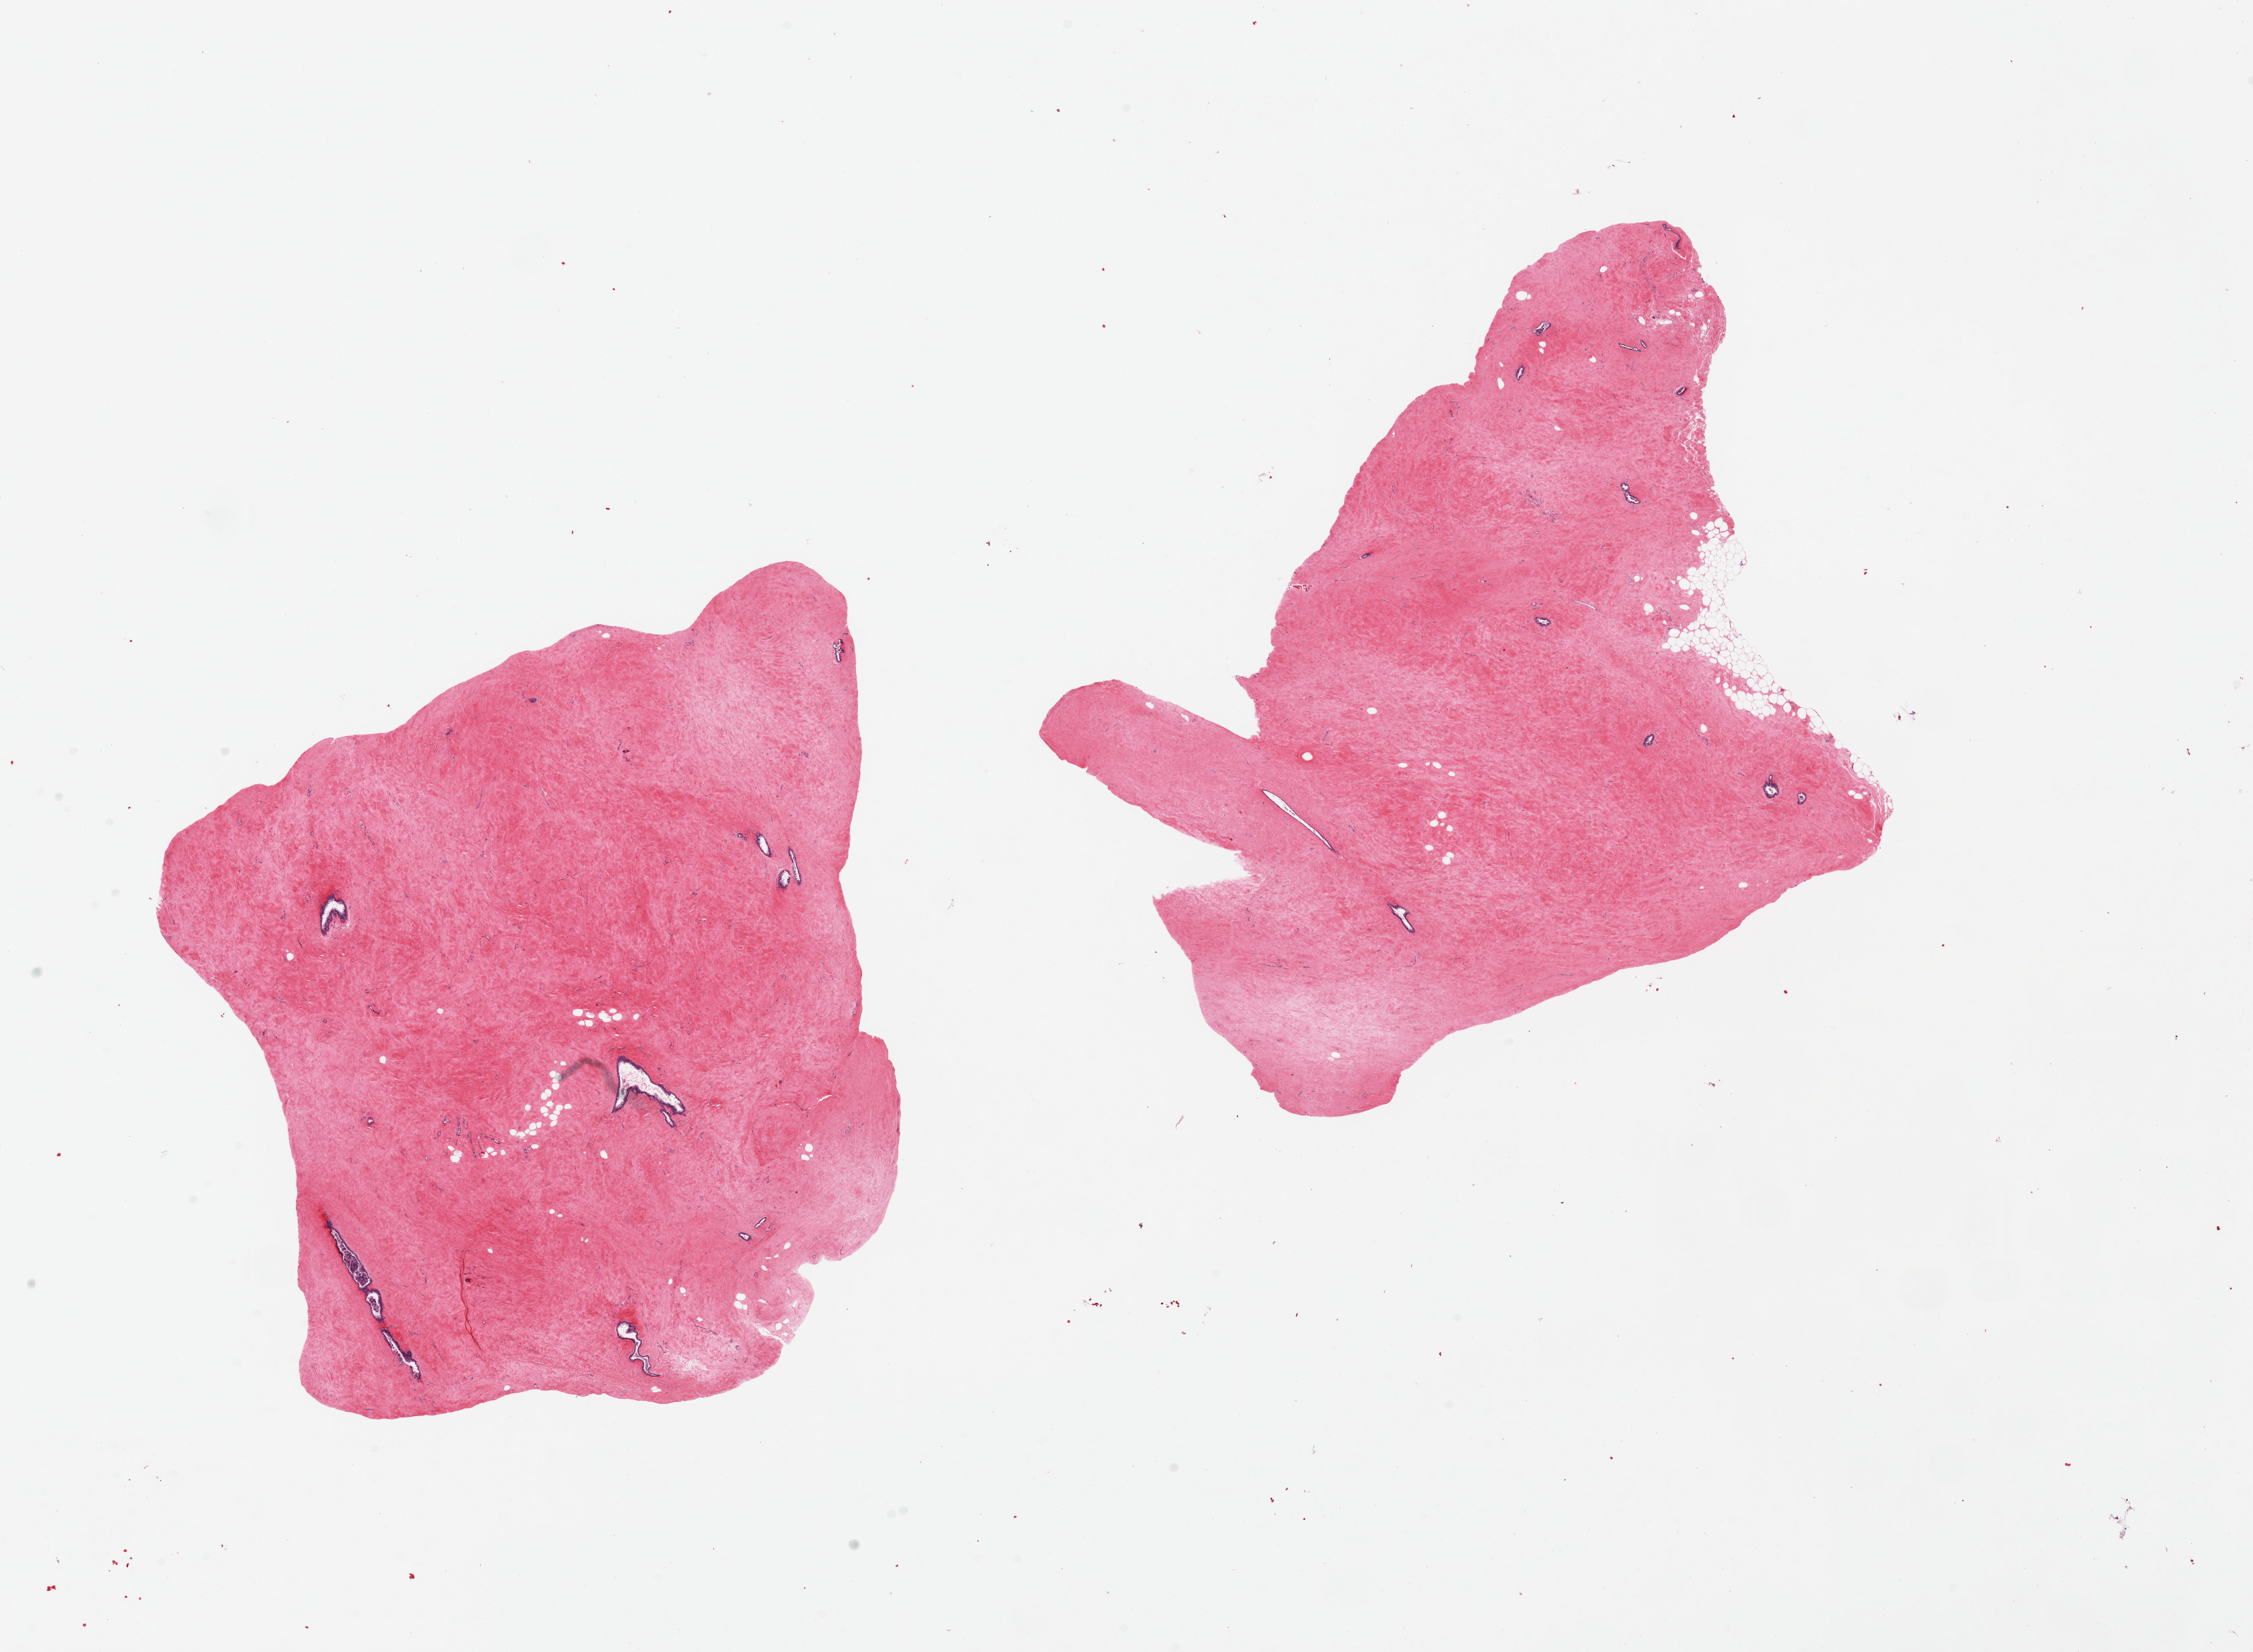
H&E whole-slide image, brightfield — a low-resolution overview of the entire scanned area, about 26.6 x 19.5 mm (slide scanned at 20x). PAXgene-fixed, paraffin-embedded tissue. Section of breast (target tissue). Tissue donor sample.
Review note (as recorded): 2 pieces. Gynecomastoid hyperplasia.